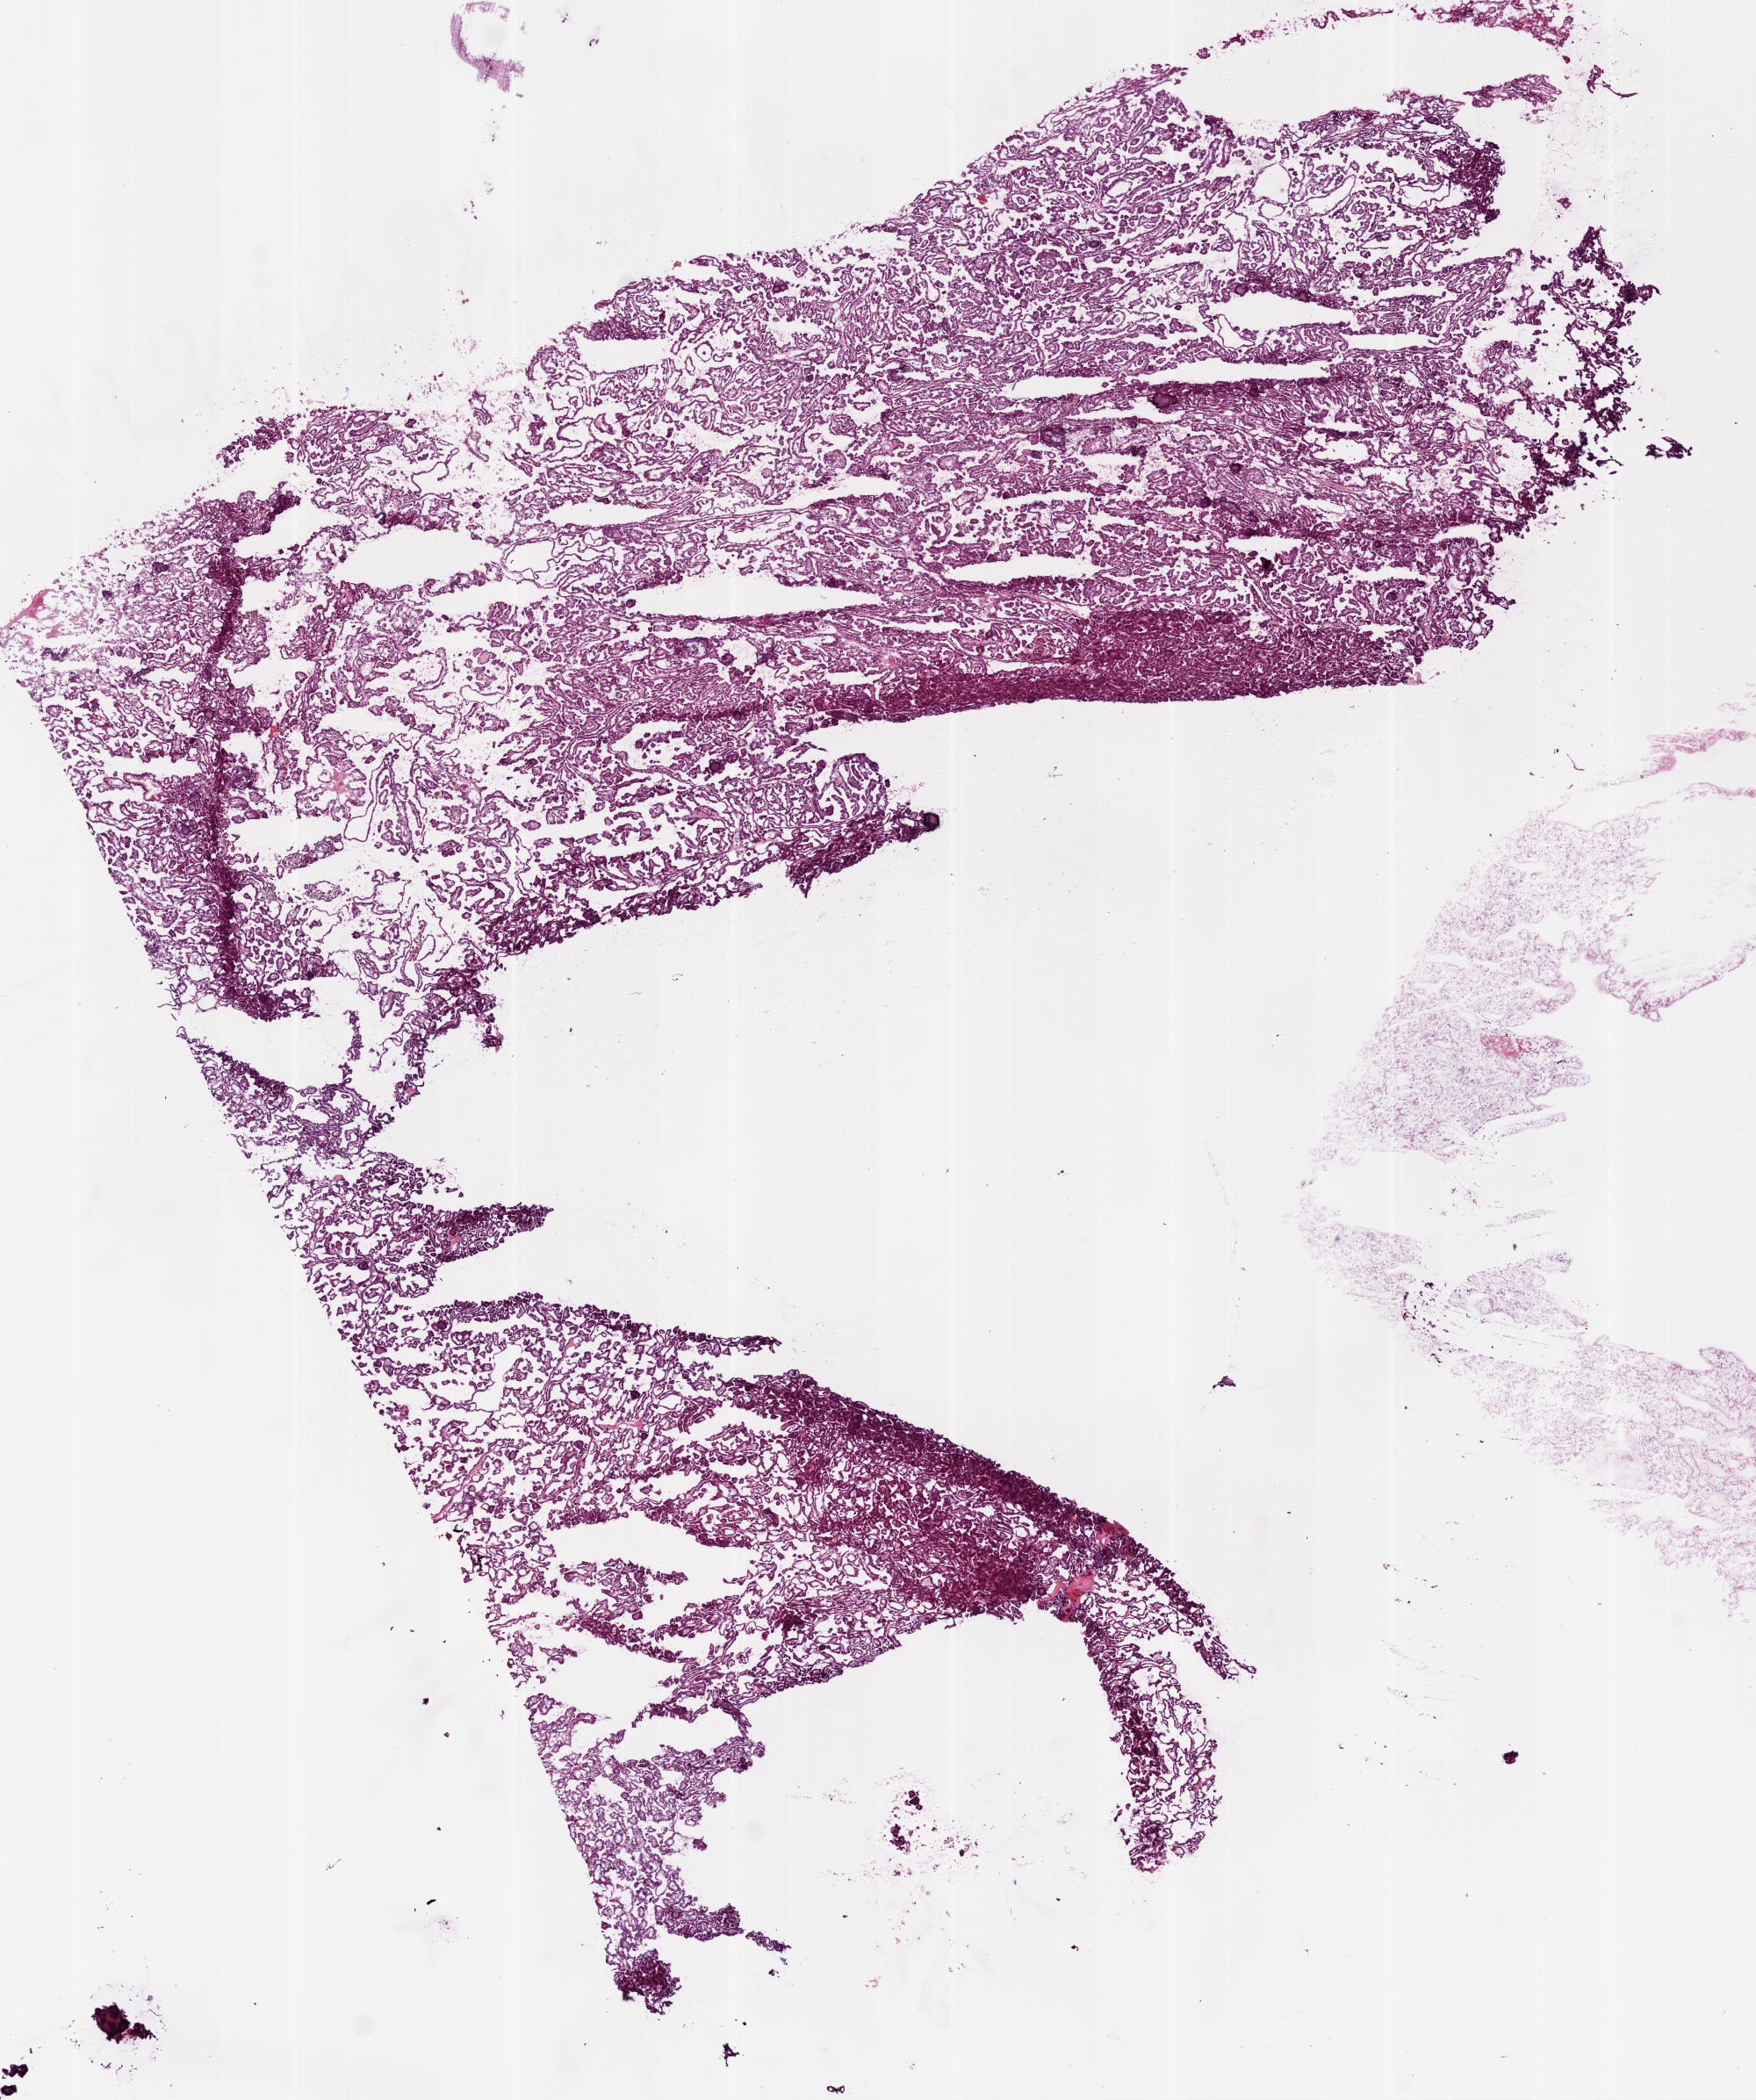
Hematoxylin and eosin (H&E) stained whole-slide image — shown as a low-resolution overview of the whole scanned area (about 8.0 x 9.6 mm, slide scanned at 20x), frozen section from the bottom of the tissue portion, kidney, primary tumour sample. Patient: male, age at initial diagnosis 74 years. Pathologist review of this section (percent, as recorded): tumour cells 87%, tumour nuclei 80%, normal cells 0%, stromal cells 10%, necrosis 3%.
• pathologic diagnosis: Papillary adenocarcinoma, NOS
• laterality: right
• AJCC pathologic stage: I